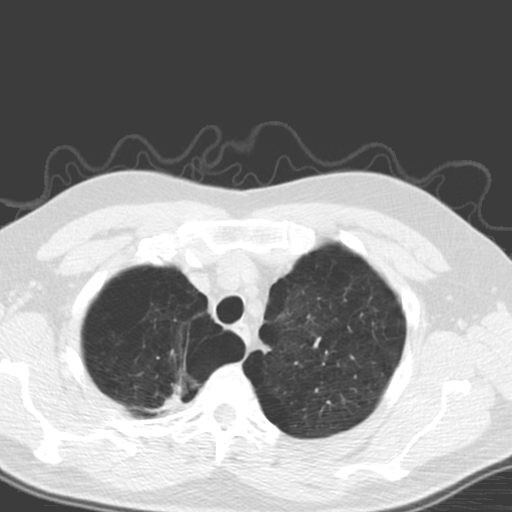
Low-dose screening chest CT, one axial slice; lung window (W 1500 / L -600 HU); 512 × 512 image matrix, field of view 340 × 340 mm.
Structures marked on this image (outlined manually by an expert reader):
- lesion 1 (tumor, upper lobe of right lung): bounding box [x1, y1, x2, y2] px = [161, 382, 183, 408]